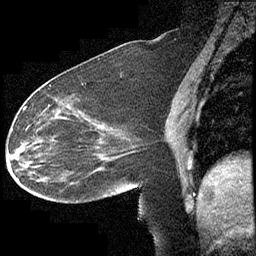
Breast MRI (dynamic contrast-enhanced), one sagittal slice; position 163 of 232 along the scan axis; dynamic contrast-enhanced study with each time point stored as its own series, time point 2 of 4 at this slice position (early post-contrast, ordered by acquisition time); 1.5 T; TE 4.2 ms, TR 6.7 ms; 256 × 256 image matrix, field of view 200 × 200 mm. Patient: female, 63 years. From the clinical record (not read from this slice): setting: breast cancer imaged before/during neoadjuvant chemotherapy; receptor status: triple-negative.
Outlined on this slice (semi-automatically segmented with operator editing):
- analysis volume of interest (the breast-tissue region the enhancement analysis was run in; not a lesion): bounding box [x1, y1, x2, y2] px = [13, 90, 140, 211]
- tumour enhancement mask (voxels above the 70 % enhancement threshold inside the analysis volume of interest): [23, 105, 50, 130]